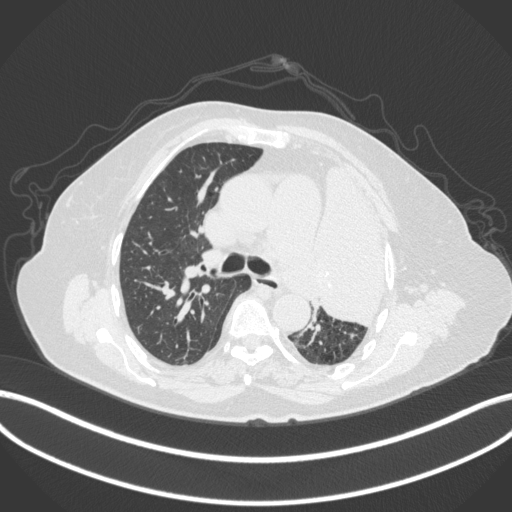
Chest CT, one axial slice. Slice 251 of 399 in the series (ordered by position). Lung window (W 1500 / L -600 HU). 512 × 512 image matrix, field of view 400 × 400 mm. Female patient, age 75 years. From the clinical record (not read from this slice): clinical TNM (as recorded): T3 N3 M1.
Structures marked on this image (bounding box drawn by a radiologist):
- lung tumour (recorded histology: adenocarcinoma): box from (x=315, y=154) to (x=396, y=329) px